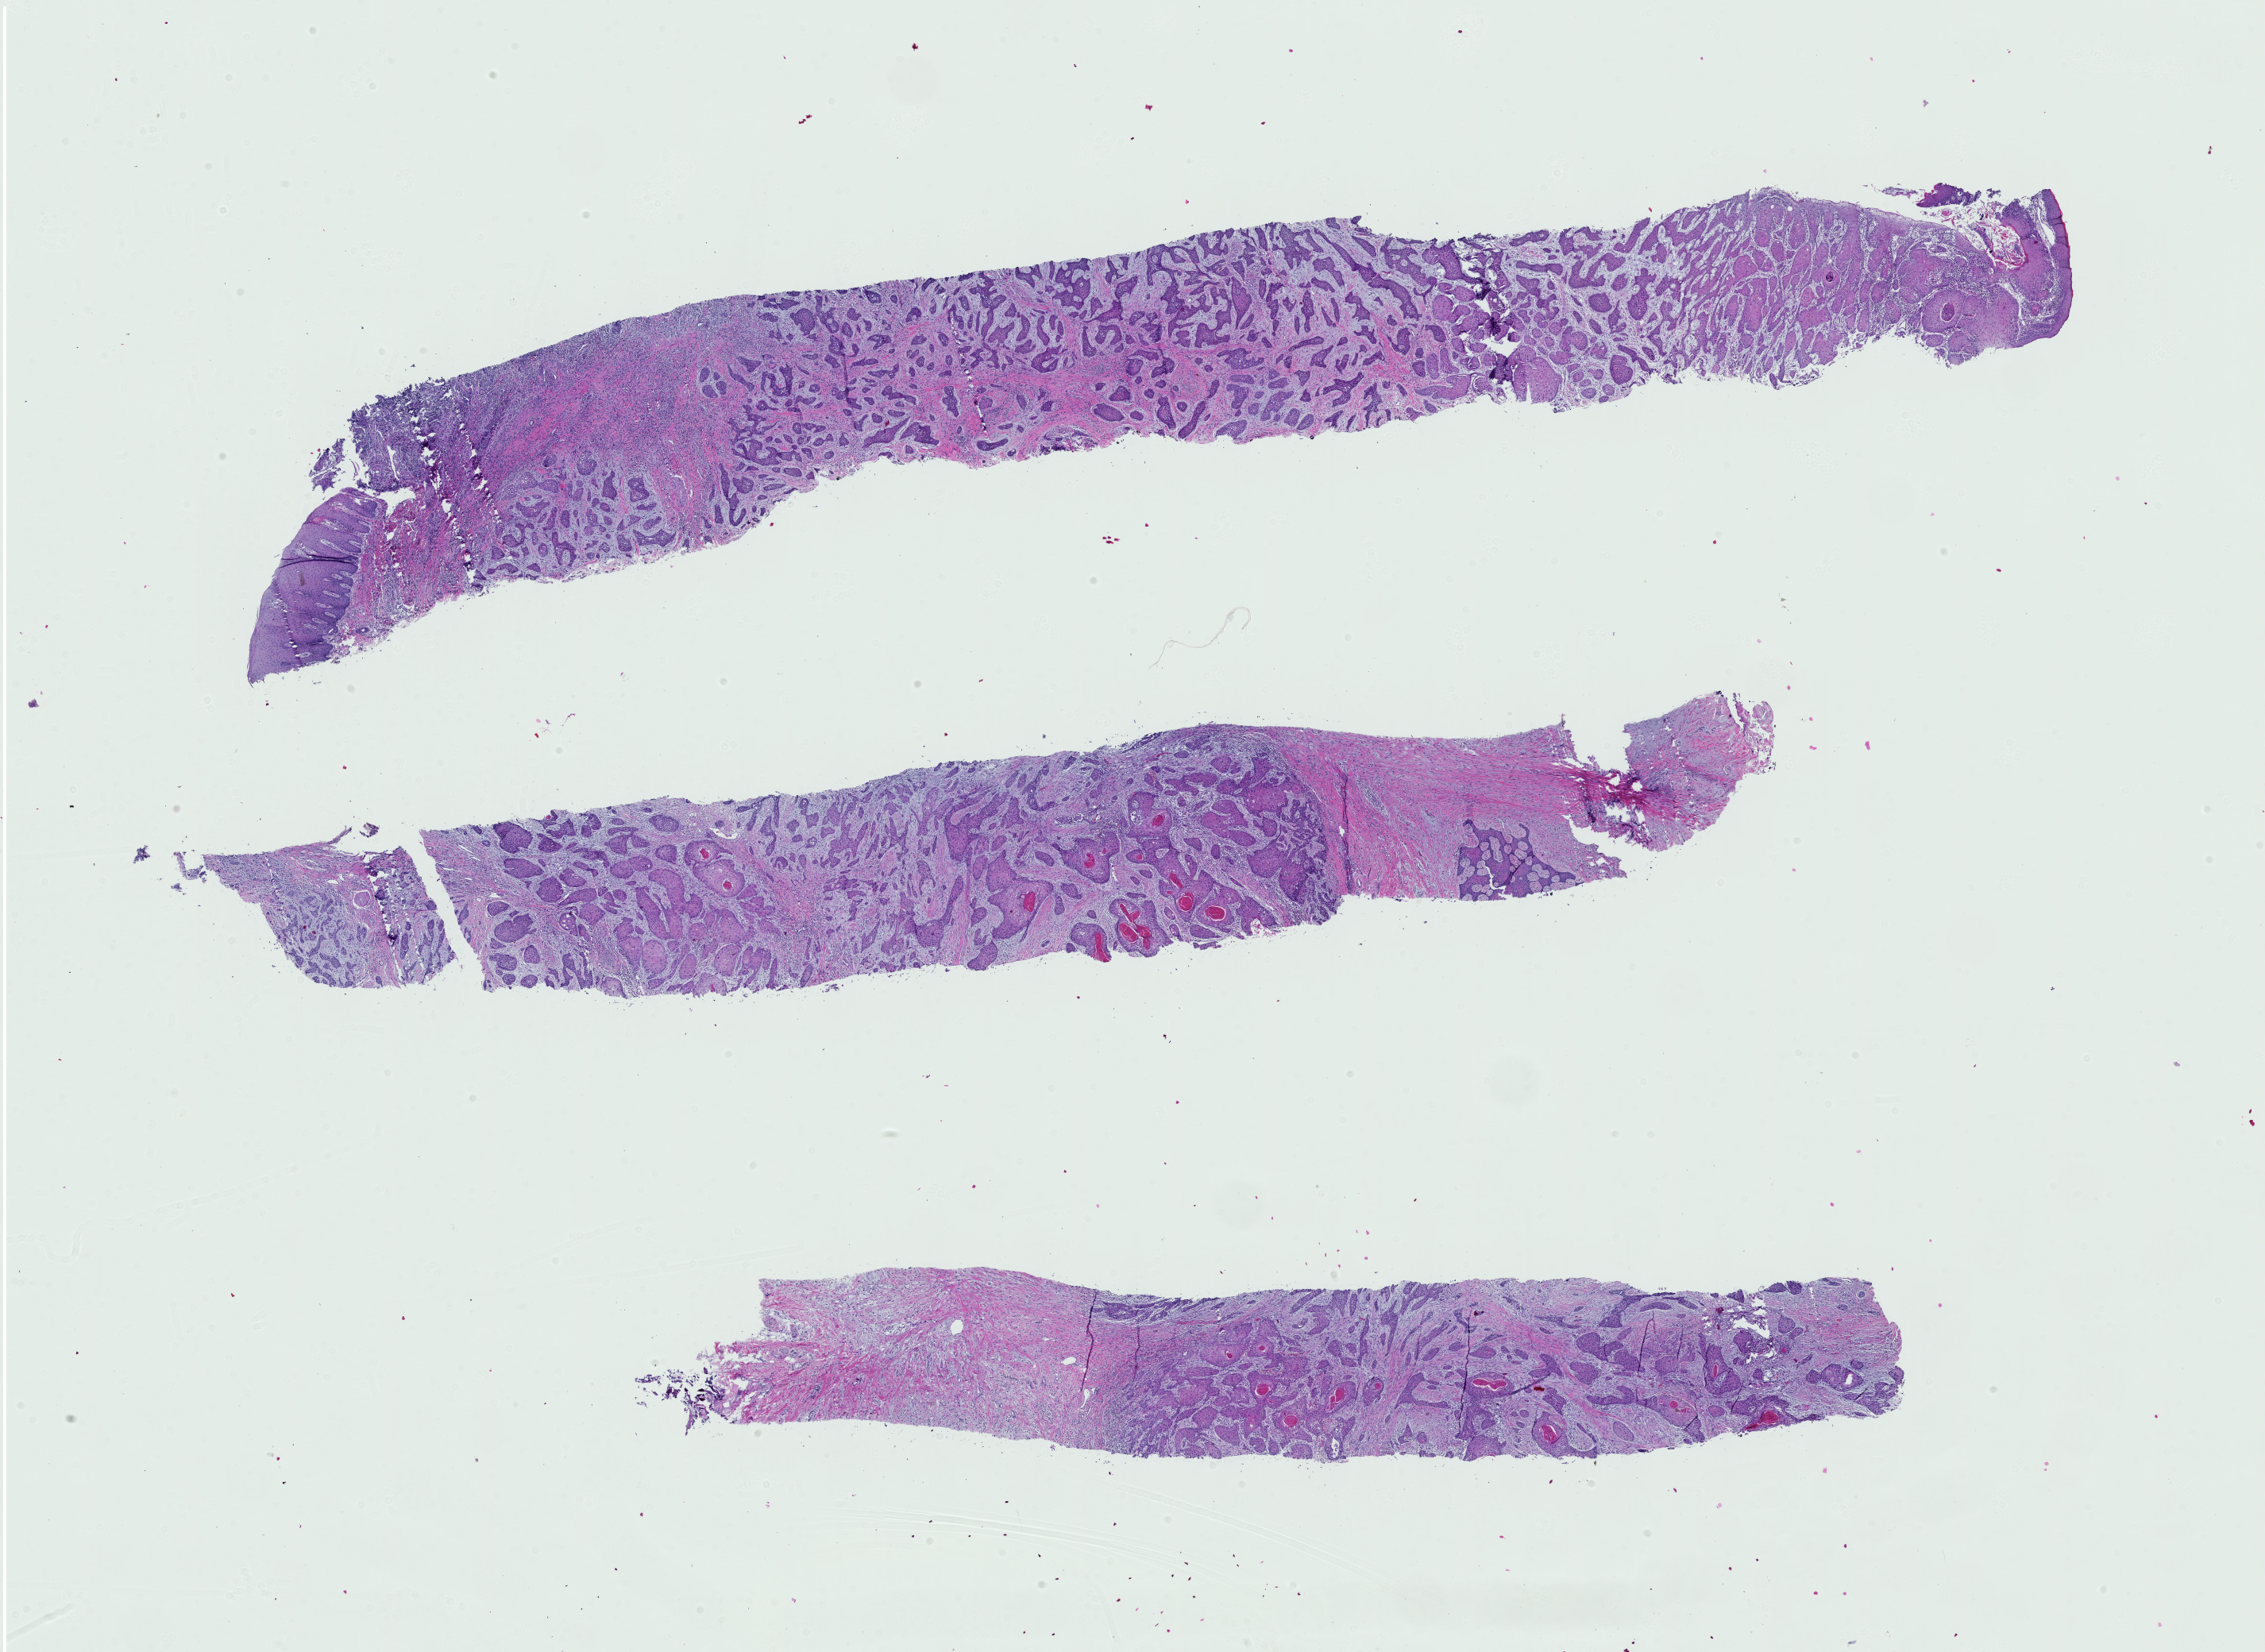
H&E whole-slide image, whole scanned area (about 20.7 x 15.1 mm, acquisition: 40x scan) shown as a low-resolution overview. Formalin-fixed paraffin-embedded (FFPE) diagnostic section. Primary tumour sample from the head and neck. Female patient; age at initial diagnosis 79 years. Histologic grade: G1 (well differentiated).
• AJCC pathologic stage: IVA (7th edition)
• diagnosis: Squamous cell carcinoma, NOS (floor of mouth, NOS)
• TNM: T4 NX MX